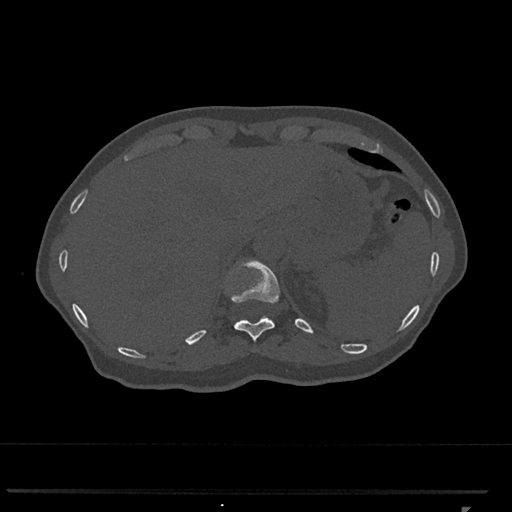
CT including the spine, one axial slice. Position 509 of 793 along the scan axis. Bone window (W 1800 / L 400 HU). 0.5 mm slice thickness. 512 × 512 image matrix, field of view 380 × 380 mm. Patient: female, 62 years. From the clinical record (not read from this slice): primary cancer: renal.
Structures marked on this image (semi-automatically segmented with operator editing):
- T11 vertebra: bounding box (x1, y1, x2, y2) in pixels: (231, 259, 280, 341)